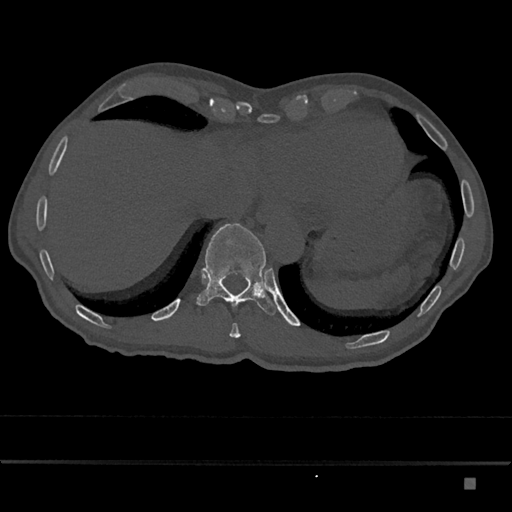
CT including the spine, one axial slice. Slice 688 of 797 in the series (ordered by position). 120 kVp. Bone window (W 1800 / L 400 HU). 512 × 512 image matrix, field of view 390 × 390 mm. Male patient, age 72 years. From the clinical record (not read from this slice): primary cancer: prostate.
Structures marked on this image (semi-automatically segmented with operator editing):
- T10 vertebra: bounding box [x1, y1, x2, y2] px = [230, 323, 240, 338]
- T11 vertebra: [196, 223, 276, 315]